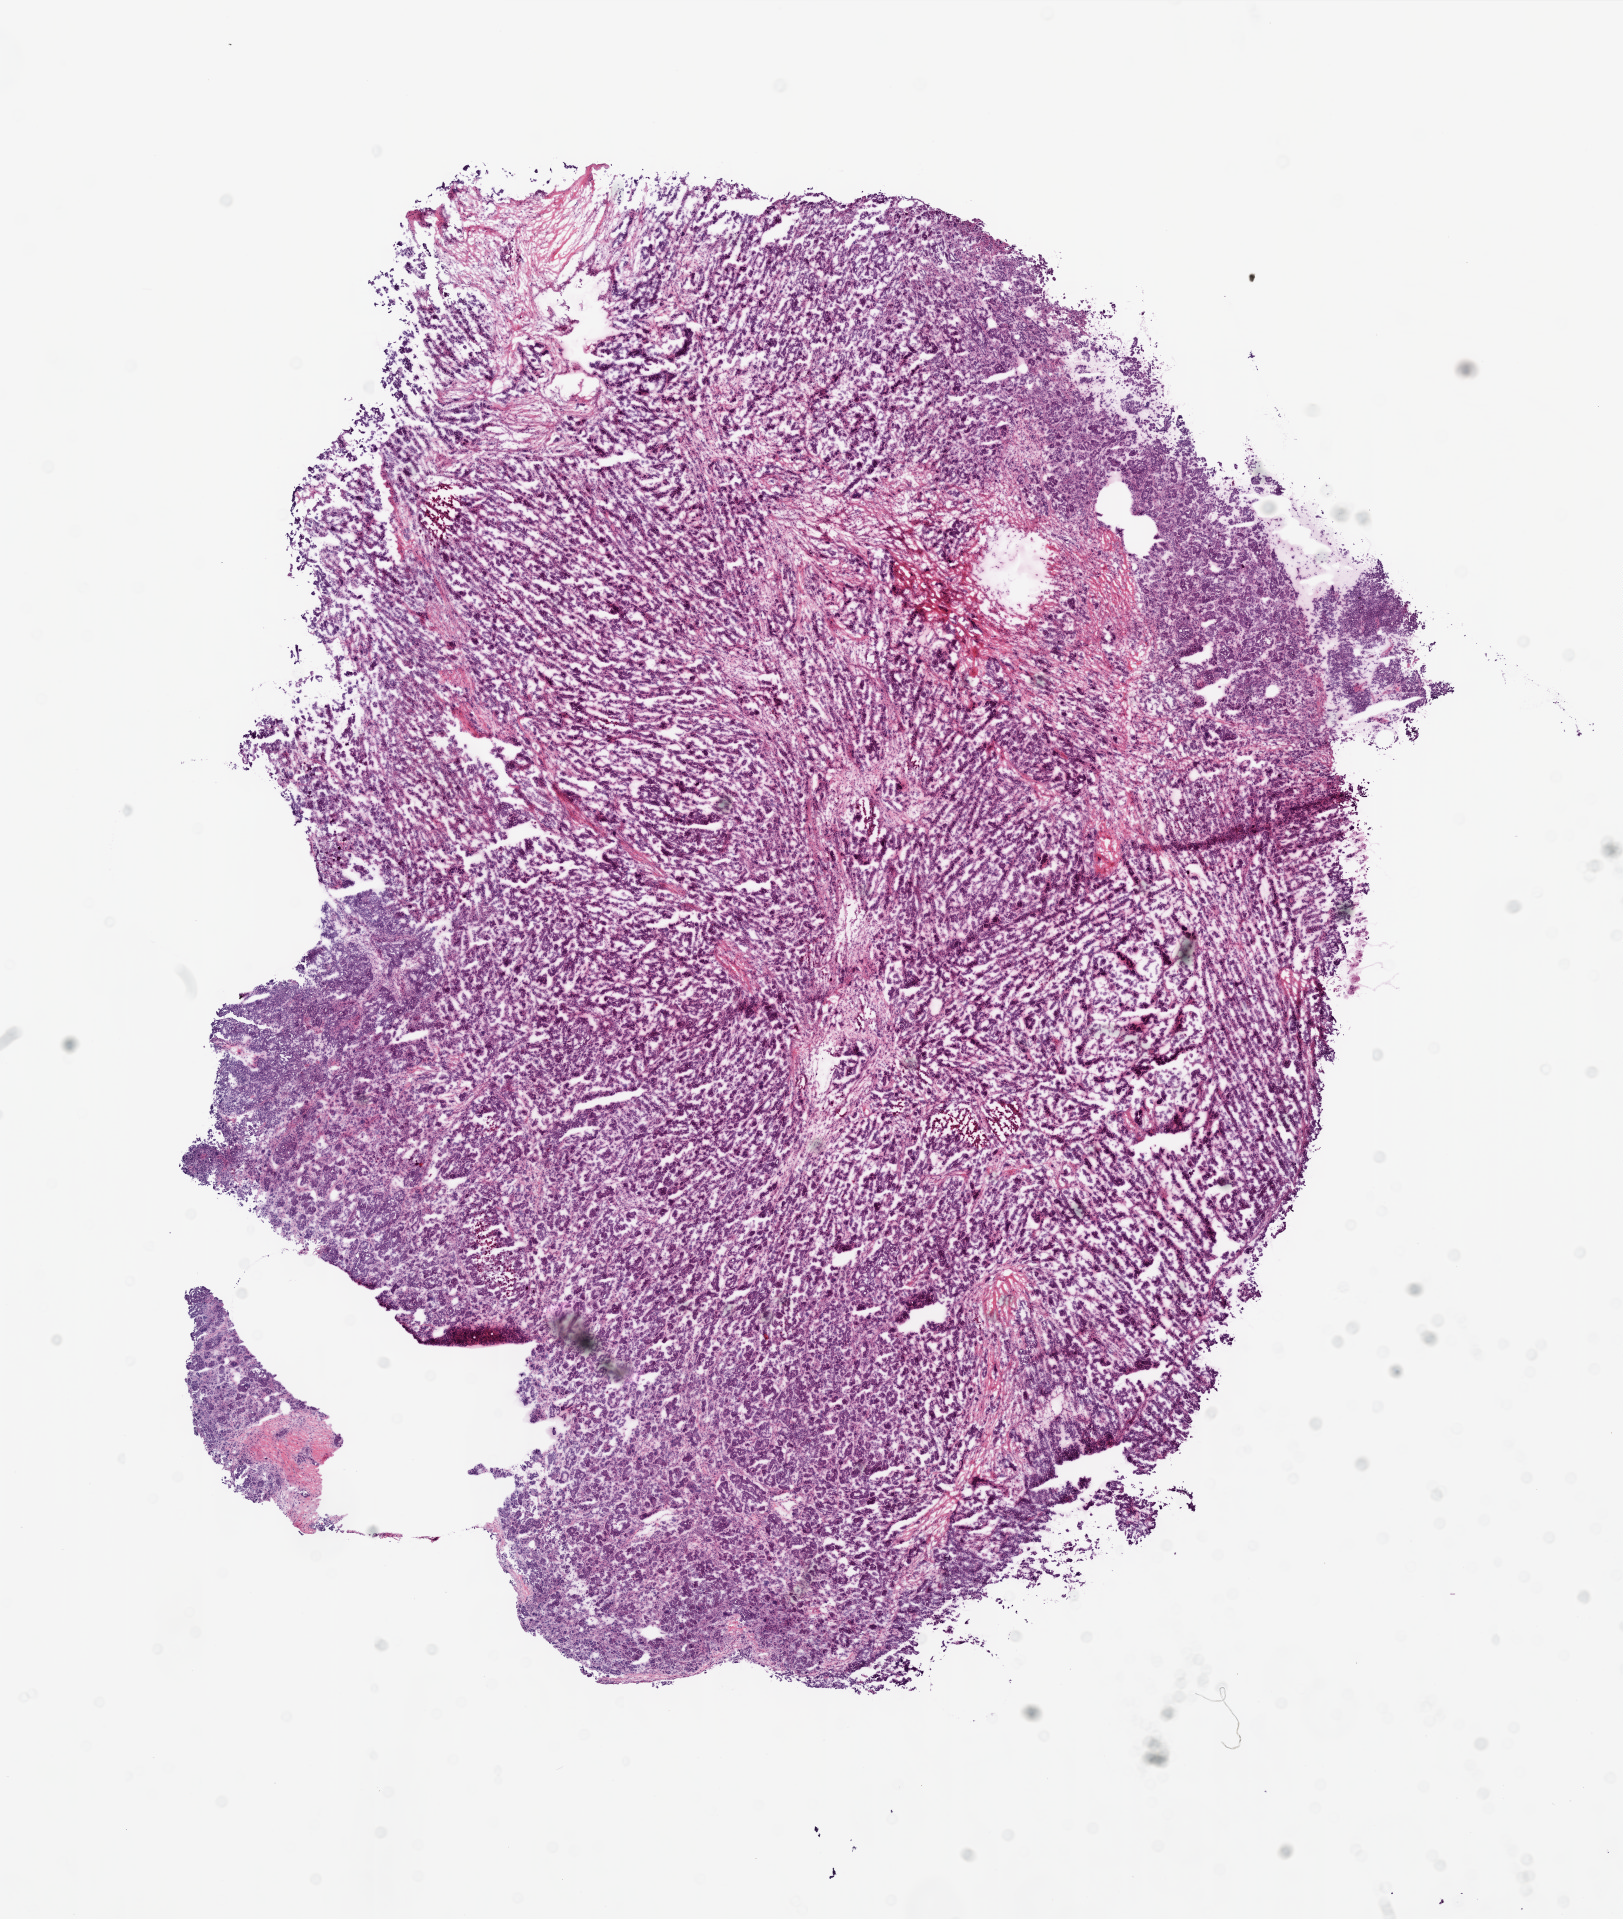
Digitized Hematoxylin and eosin (H&E) stained tissue section (whole slide) — low-resolution overview of the scanned area, about 13.0 x 15.4 mm (acquisition: 20x scan); frozen section from the top of the tissue portion; ovary, primary tumour sample. Patient: female, age at initial diagnosis 54 years. Histologic grade: G3 (poorly differentiated). Slide review estimates, as recorded: tumour cells 89%, tumour nuclei 90%, normal cells 10%, stromal cells 0%, necrosis 1%.
• FIGO stage: IIIC
• laterality: right
• diagnosis: Serous cystadenocarcinoma, NOS